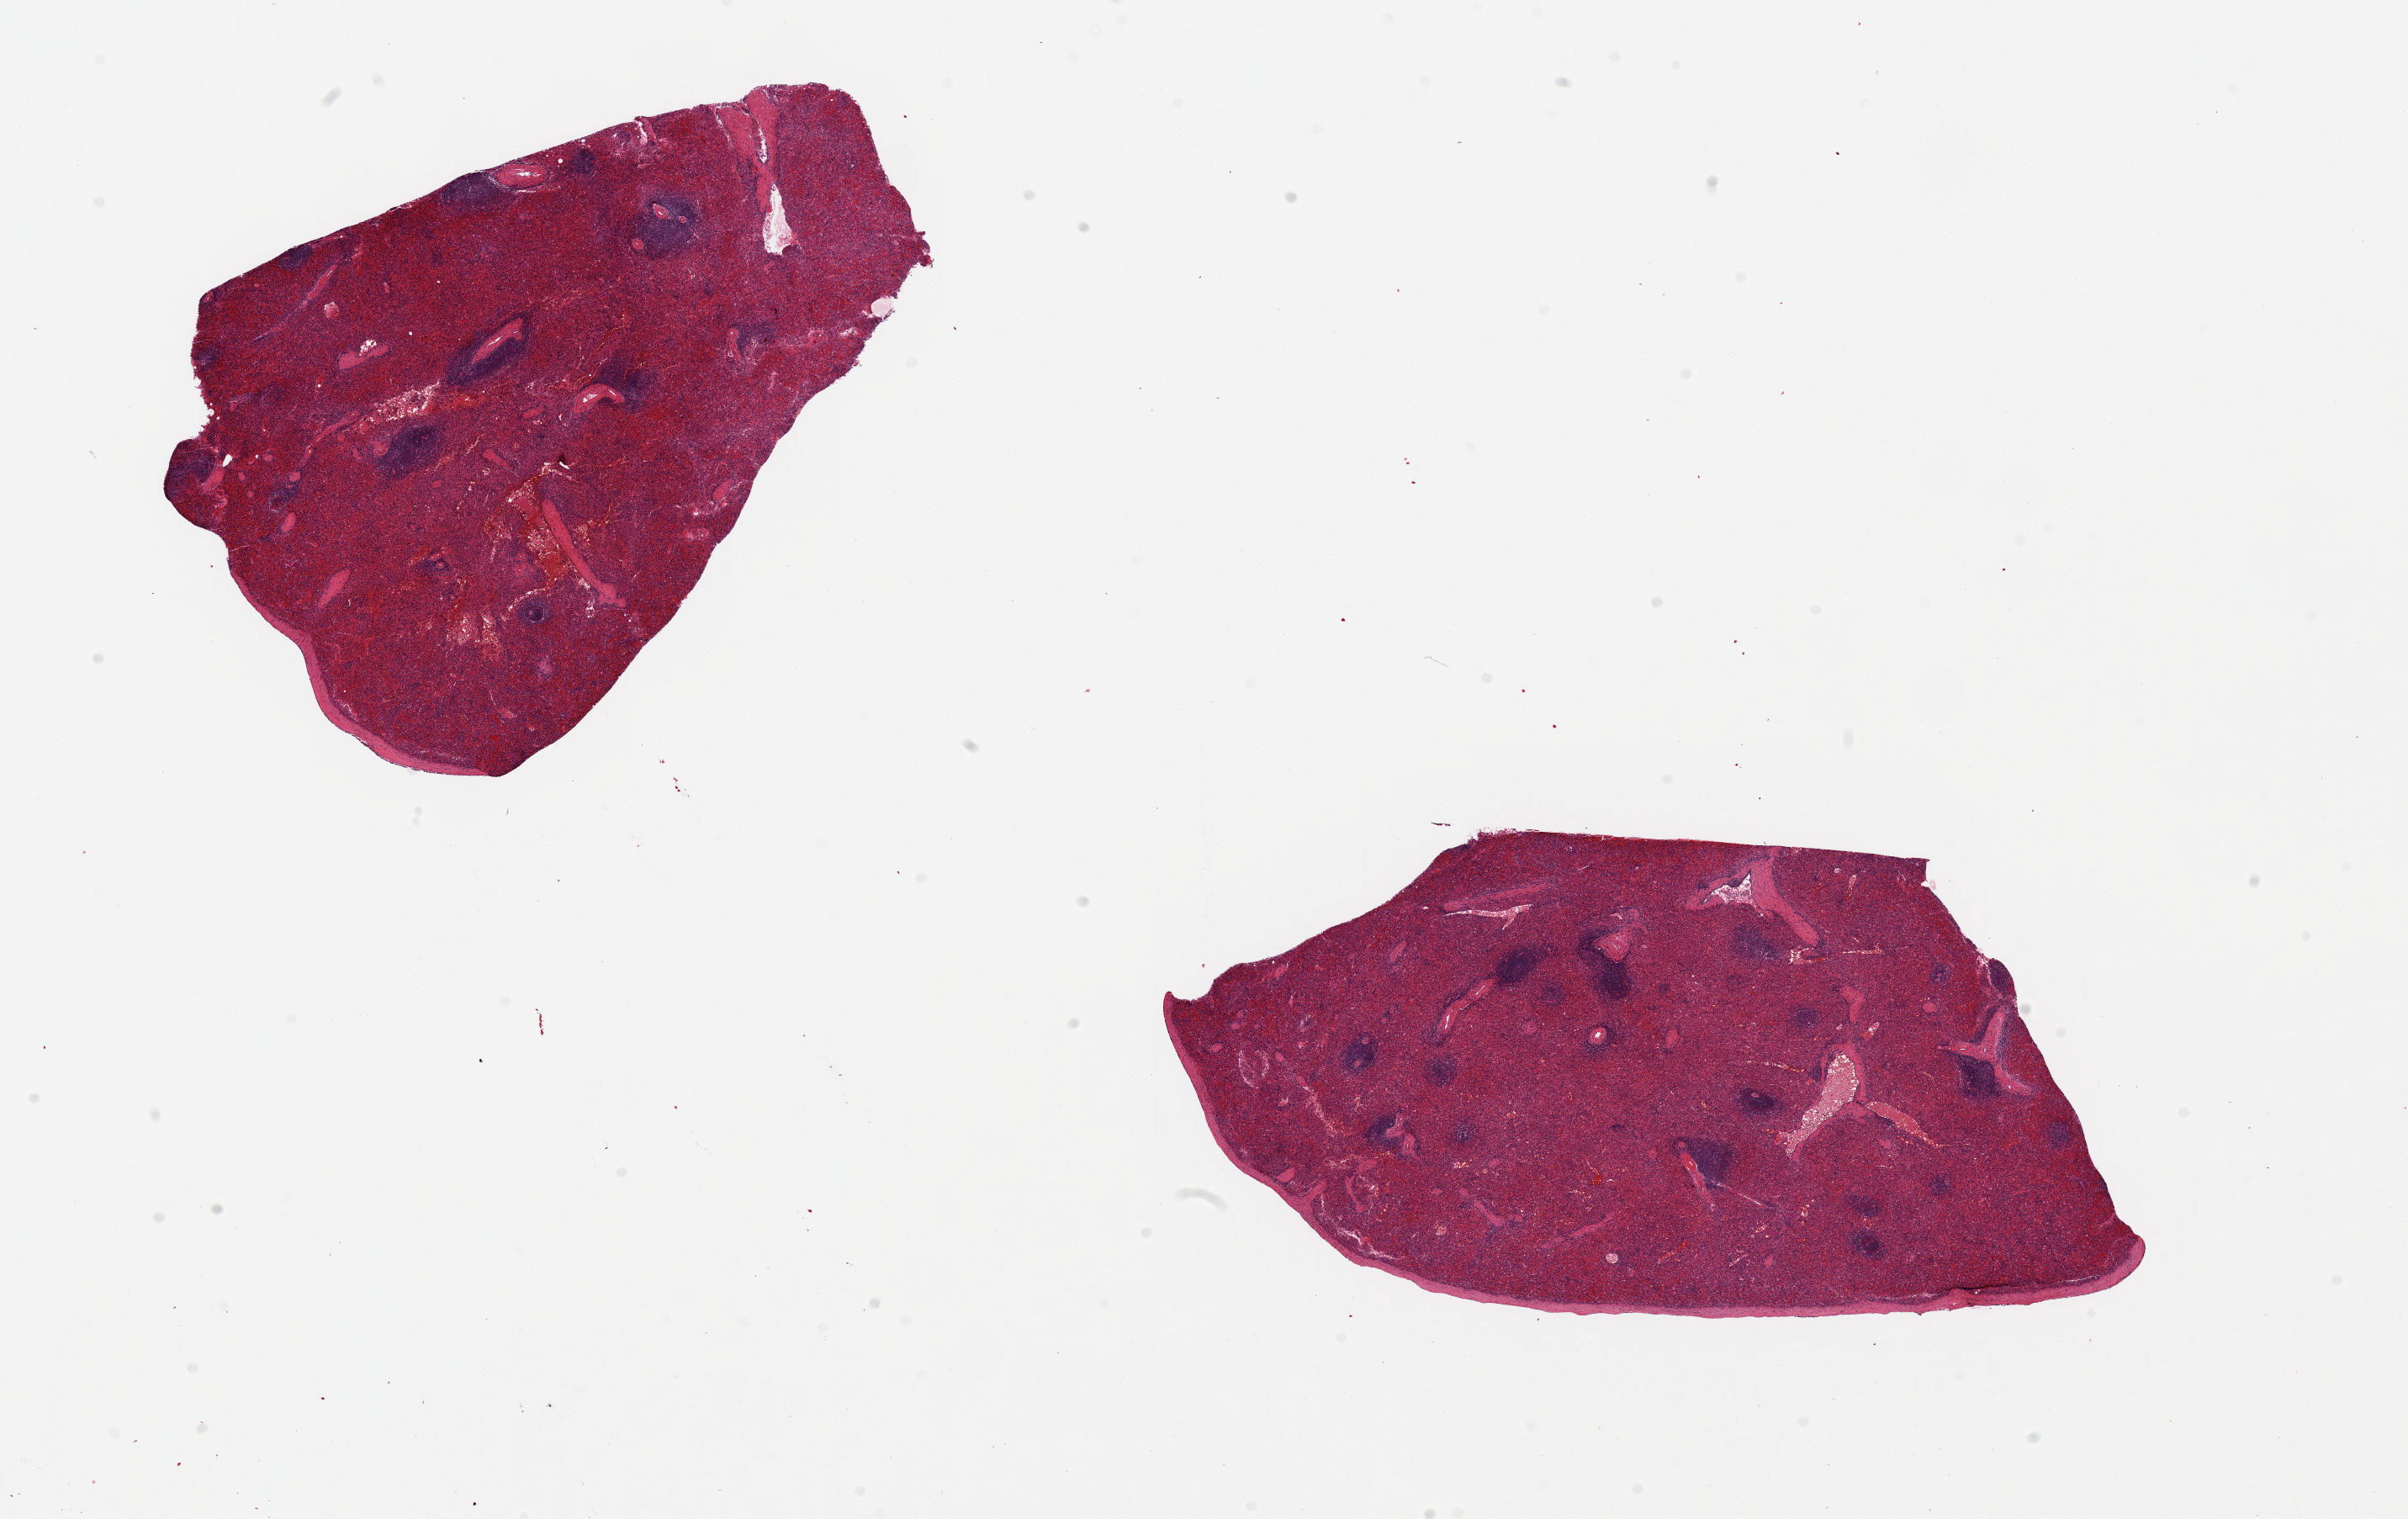
Digitized haematoxylin and eosin-stained section — shown as a low-resolution overview of the whole scanned area (about 22.6 x 14.3 mm, from a 20x scan). PAXgene-fixed, paraffin-embedded tissue. Section of spleen (target tissue). Donor tissue sample. Male donor.
Review note (as recorded): 2 ~8x5mm pieces.